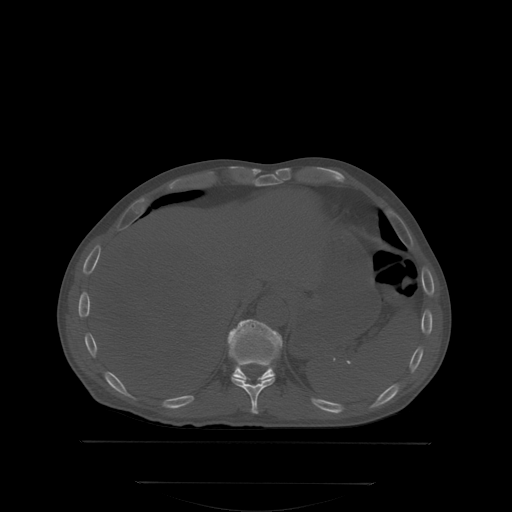
CT including the spine, one axial slice. Slice 188 of 350 in the series (ordered by position). Bone window (W 1800 / L 400 HU). 512 × 512 image matrix, field of view 500 × 500 mm. Patient: male, 58 years. Case-level facts recorded for this patient, not image findings: primary cancer: prostate.
Annotated regions visible in this slice (semi-automatically segmented with operator editing):
- T10 vertebra: box from (x=231, y=376) to (x=276, y=413) px
- T11 vertebra: (x=229, y=320)–(x=281, y=381)